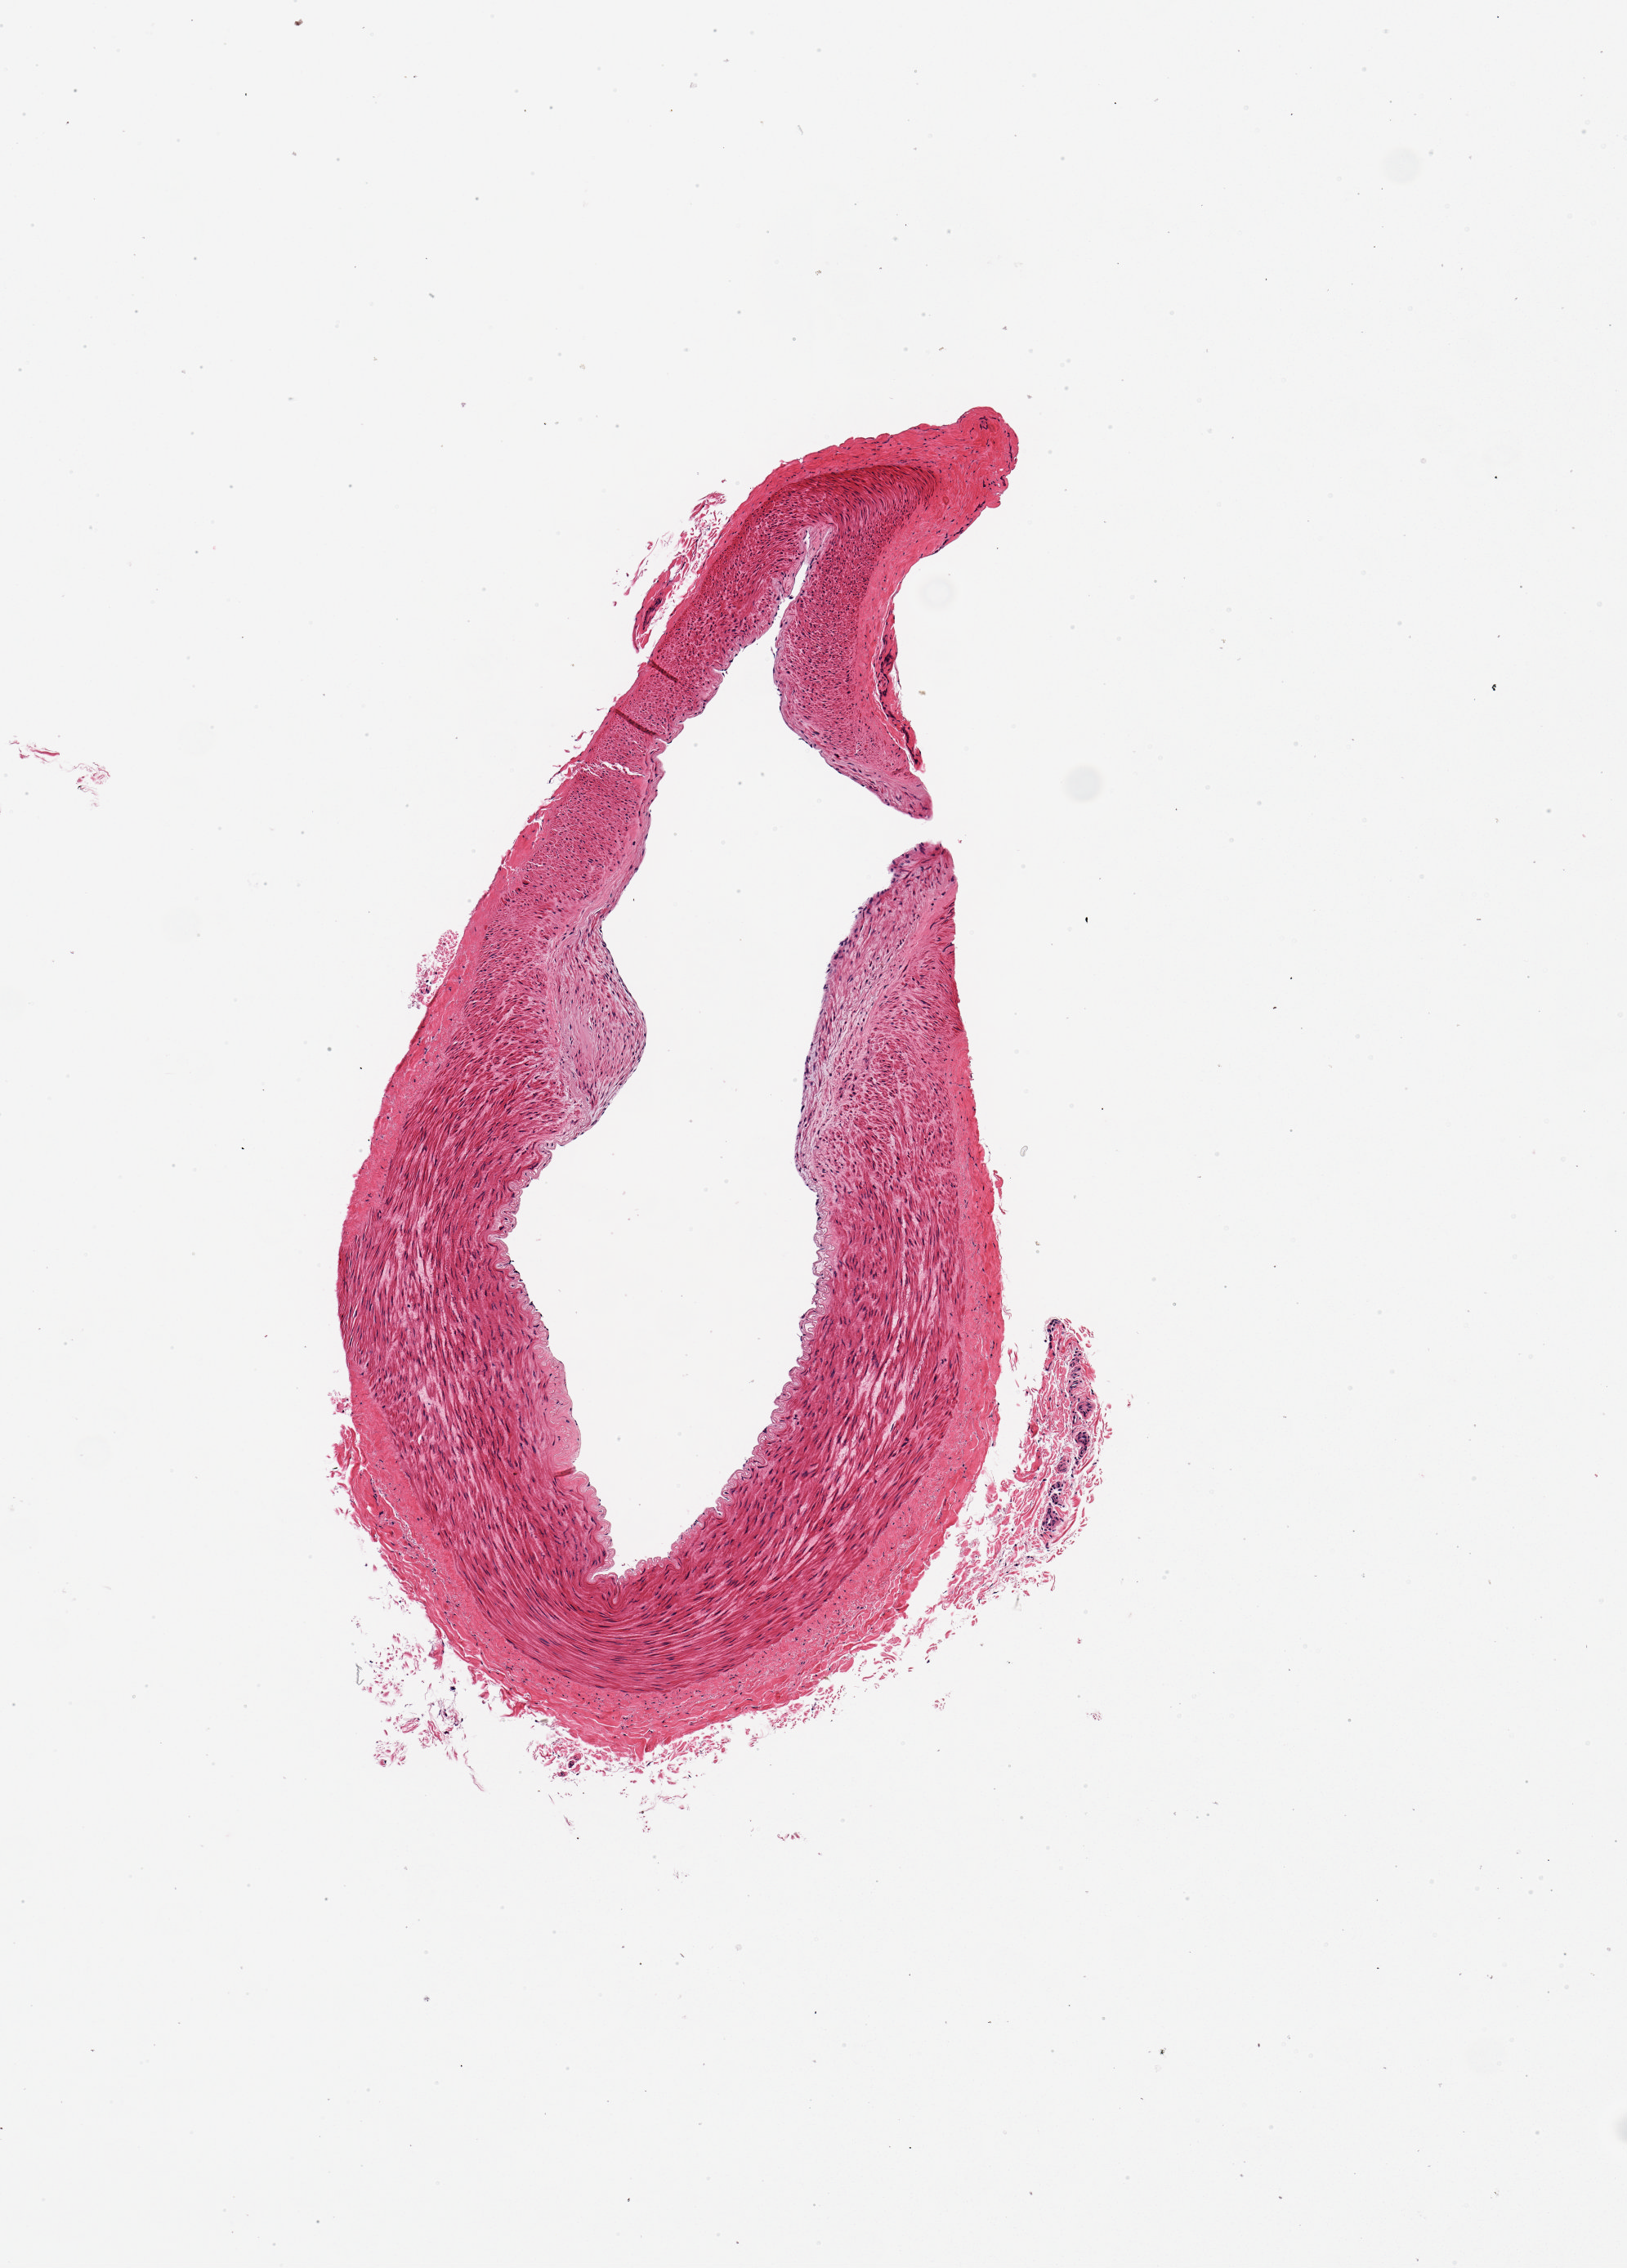
H&E whole-slide image, low-resolution overview of the scanned area, about 3.9 x 5.5 mm (slide scanned at 20x), PAXgene-fixed paraffin-embedded (PFPE) section, sampled site (target tissue): tibial nerve, tissue donor sample. Donor sex: male.
- reviewer comment on this tissue sample: 1 piece; artery not nerve